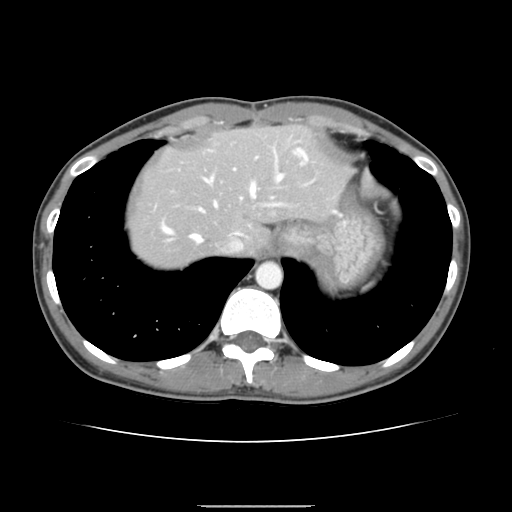
Contrast-enhanced abdominal CT, one axial slice; position 122 of 150 along the scan axis; intravenous contrast given; soft-tissue window (W 400 / L 40 HU); 2.5 mm slice thickness; 512 × 512 image matrix, field of view 324 × 324 mm. Female patient, age 32 years. From the clinical record (not read from this slice): diagnosis: colorectal cancer liver metastases, imaged before liver resection; multiple liver metastases: yes.
Annotated regions visible in this slice (outlined manually by an expert reader):
- hepatic veins: bounding box <161,151,297,252> (left, top, right, bottom; pixels)
- liver: <128,126,349,267>
- planned liver remnant (the part of the liver to remain after resection): <128,126,349,257>
- portal vein (with intrahepatic branches): <198,148,310,212>